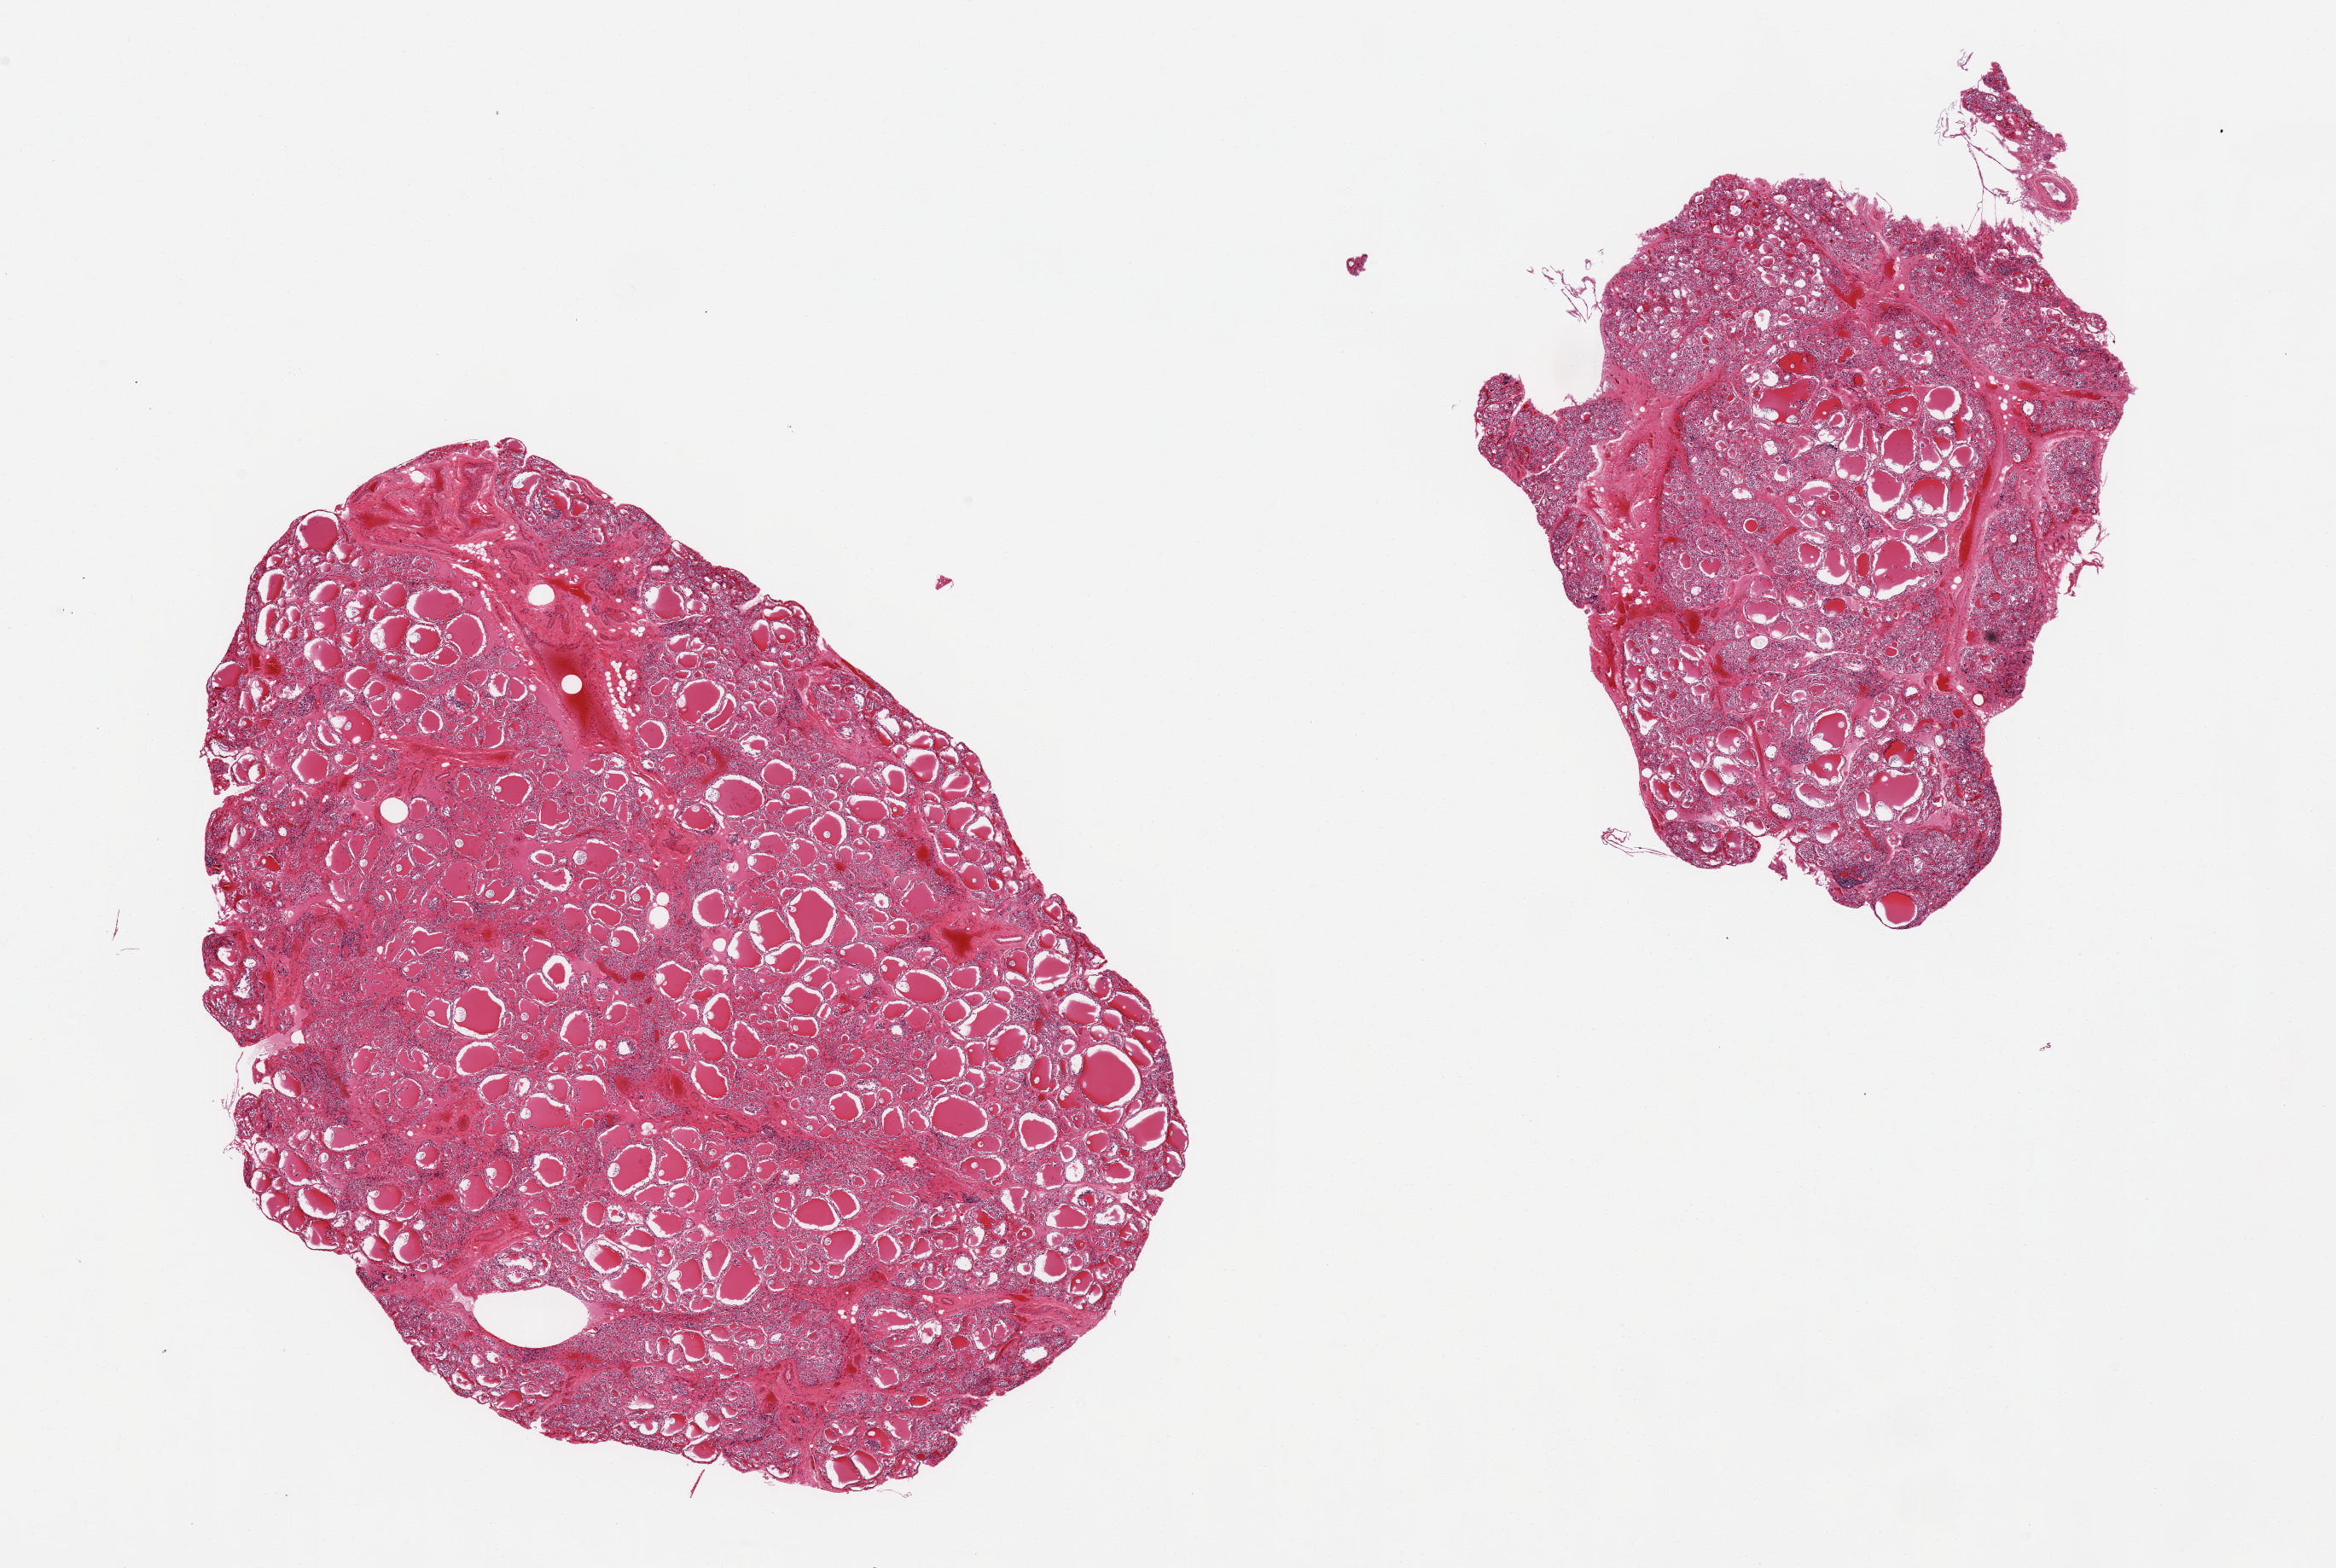
Whole-slide image, haematoxylin and eosin stain — shown as a low-resolution overview of the whole scanned area (about 21.7 x 14.5 mm), PAXgene-fixed, paraffin-embedded tissue, sampled site (target tissue): thyroid, tissue donor sample. Donor sex: male.
- review note (as recorded): 2 pieces, diffuse micronodular goitre with regressive changes/fibrosis